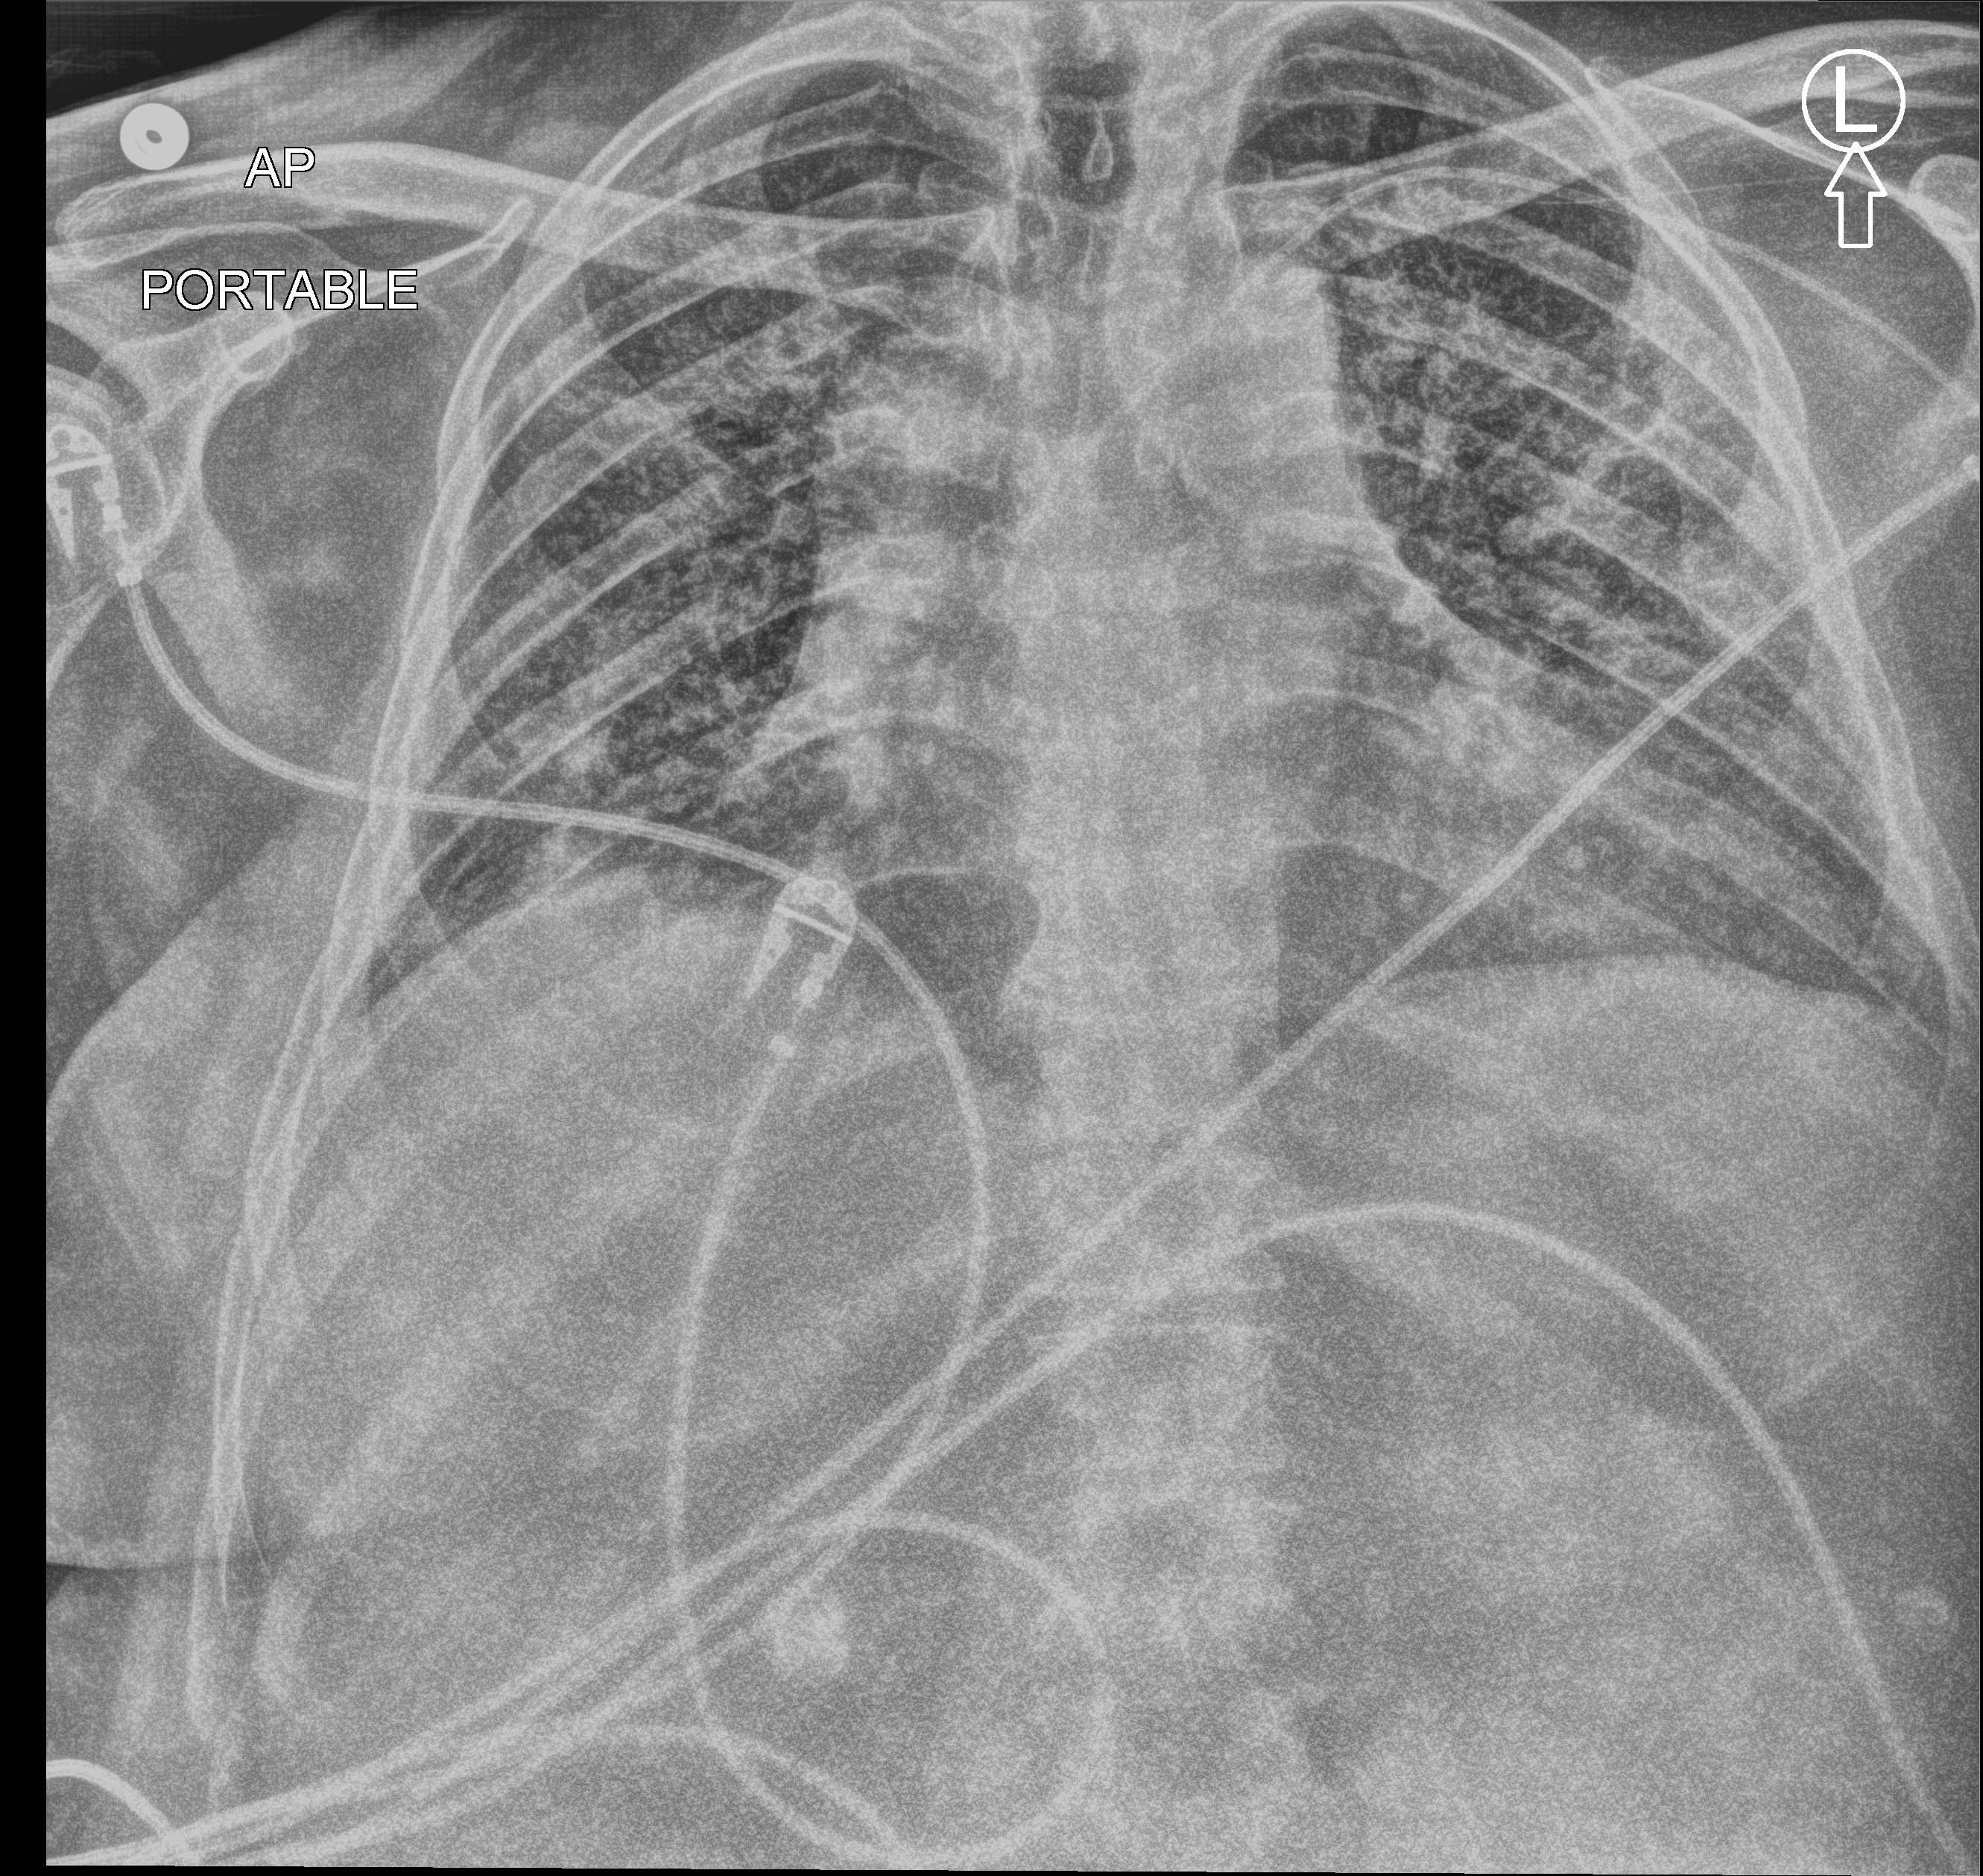
Portable chest radiograph; anteroposterior (AP) projection. Patient hospitalised with COVID-19; male, aged 18–59 years.
From the hospital-stay record, not from the radiograph (when in the stay this image was taken is not recorded):
- mechanically ventilated during this hospital stay: yes
- diabetes (admission record): no
- admitted to intensive care during this hospital stay: yes